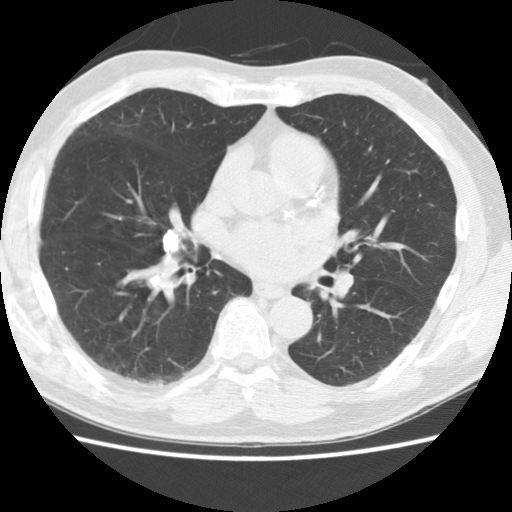
Chest CT (low-dose screening protocol), one axial image, baseline annual screen, lung window (W 1500 / L -600 HU), 2.5 mm slice thickness, standard (soft-tissue) reconstruction kernel (STANDARD), slice 68 of 116 in the series, 512 × 512 image matrix, field of view 340 × 340 mm. Male participant, aged 66 years at enrolment.
• Expert-annotated lung lesion, bounding box <139,210,196,264> (left, top, right, bottom; pixels).
• Screening reader's record for this exam: no non-calcified nodule ≥4 mm recorded.
• Lung cancer was diagnosed 314 days after this screen: large cell neuroendocrine carcinoma, right middle lobe, poorly differentiated (G3), stage IIIA (AJCC 6th edition), 15 mm at pathology.